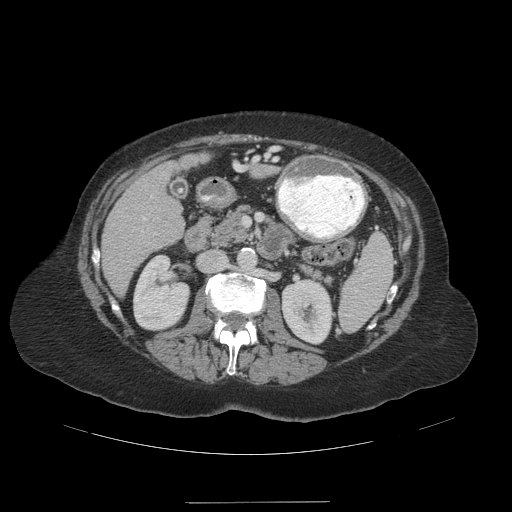
Contrast-enhanced abdominal CT (liver protocol), one axial slice. Position 48 of 99 along the scan axis. Reconstruction kernel STANDARD. Soft-tissue window (W 400 / L 40 HU). 512 × 512 image matrix, field of view 440 × 440 mm. Case-level facts recorded for this patient, not image findings: diagnosis: hepatocellular carcinoma (patient treated with transarterial chemoembolisation; whether this scan precedes or follows treatment is not stated here); TNM stage (as recorded): Stage-IVA.
Structures marked on this image (semi-automatic segmentation, software-assisted and operator-edited):
- liver parenchyma outside the tumour (the mass and vessels are separate outlines, so this box may not span the whole liver): bounding box [x1, y1, x2, y2] px = [102, 162, 184, 296]
- liver vessels: [142, 196, 152, 232]